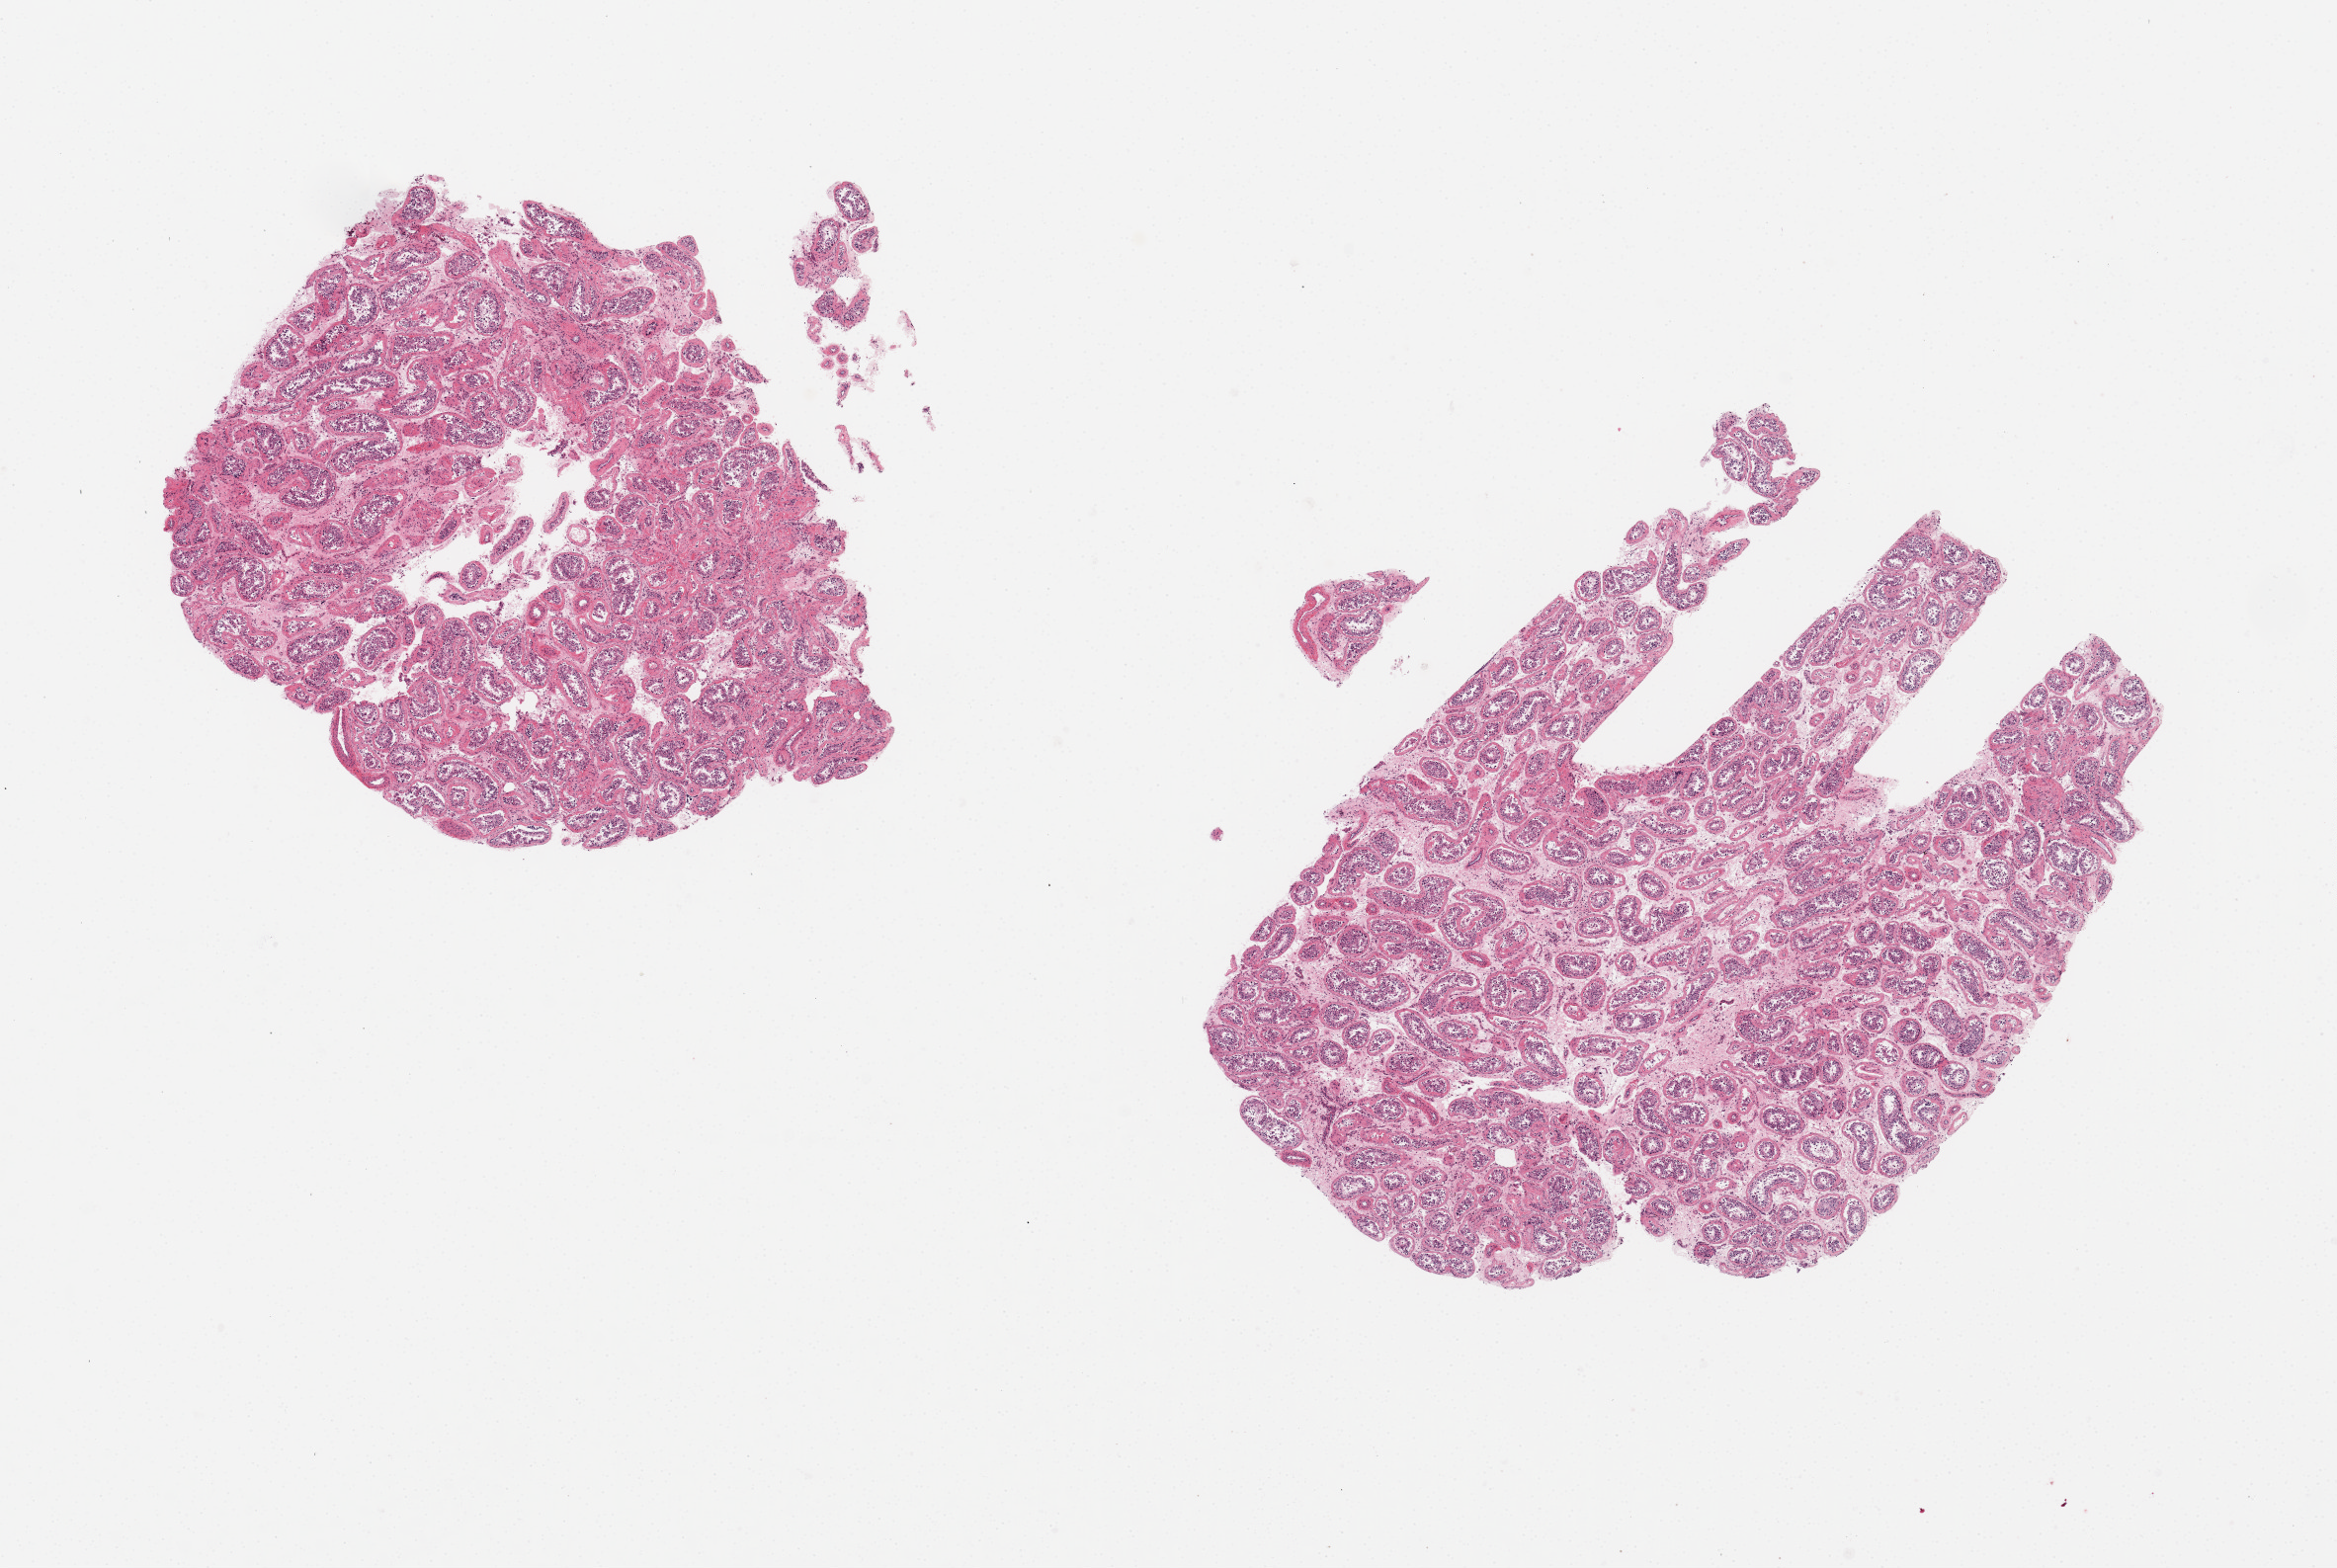
Whole-slide image, hematoxylin and eosin (H&E) stain — shown as a low-resolution overview of the whole scanned area (about 18.7 x 12.6 mm), PAXgene-fixed, paraffin-embedded tissue, section of testis (target tissue), tissue donor sample. Male donor.
- reviewer comment on this tissue sample: 2 pieces, 7x7 & 6x6mm; reduced spermatogenesis; patchy tubular fibrosis